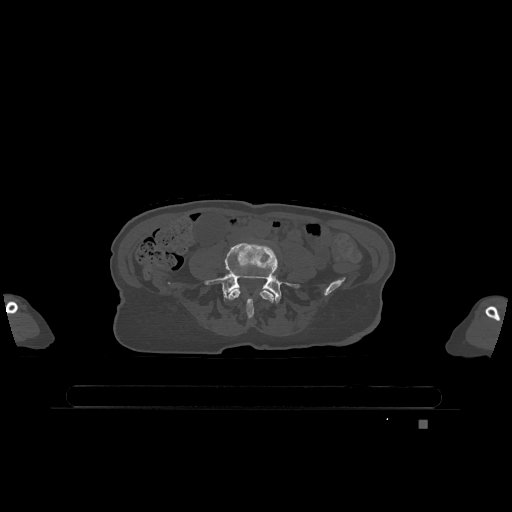
CT including the spine, one axial slice. Position 261 of 1317 along the scan axis. Bone window (W 1800 / L 400 HU). 0.5 mm slice thickness. 512 × 512 image matrix, field of view 500 × 500 mm. Patient: female, 74 years. From the clinical record (not read from this slice): primary cancer: lung; vertebrae with lytic lesions (as recorded): T1, T4, T5, T6, L4, L5.
Outlined on this slice (semi-automatic segmentation, software-assisted and operator-edited):
- L4 vertebra: bounding box [x1, y1, x2, y2] px = [226, 289, 274, 319]
- L5 vertebra: [204, 243, 299, 304]